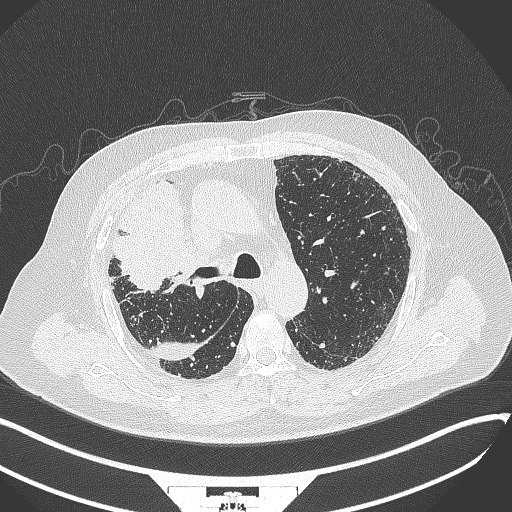
Chest CT, one axial slice. Reconstruction kernel B70f. 120 kVp. Lung window (W 1500 / L -600 HU). 1 mm slice thickness. 512 × 512 image matrix, field of view 400 × 400 mm. Male patient, age 69 years. Case-level facts recorded for this patient, not image findings: clinical TNM (as recorded): T4 N3 M1.
Outlined on this slice (rectangle marked by the reading radiologist):
- lung tumour (recorded histology: adenocarcinoma): bounding box (x1, y1, x2, y2) in pixels: (106, 174, 197, 294)